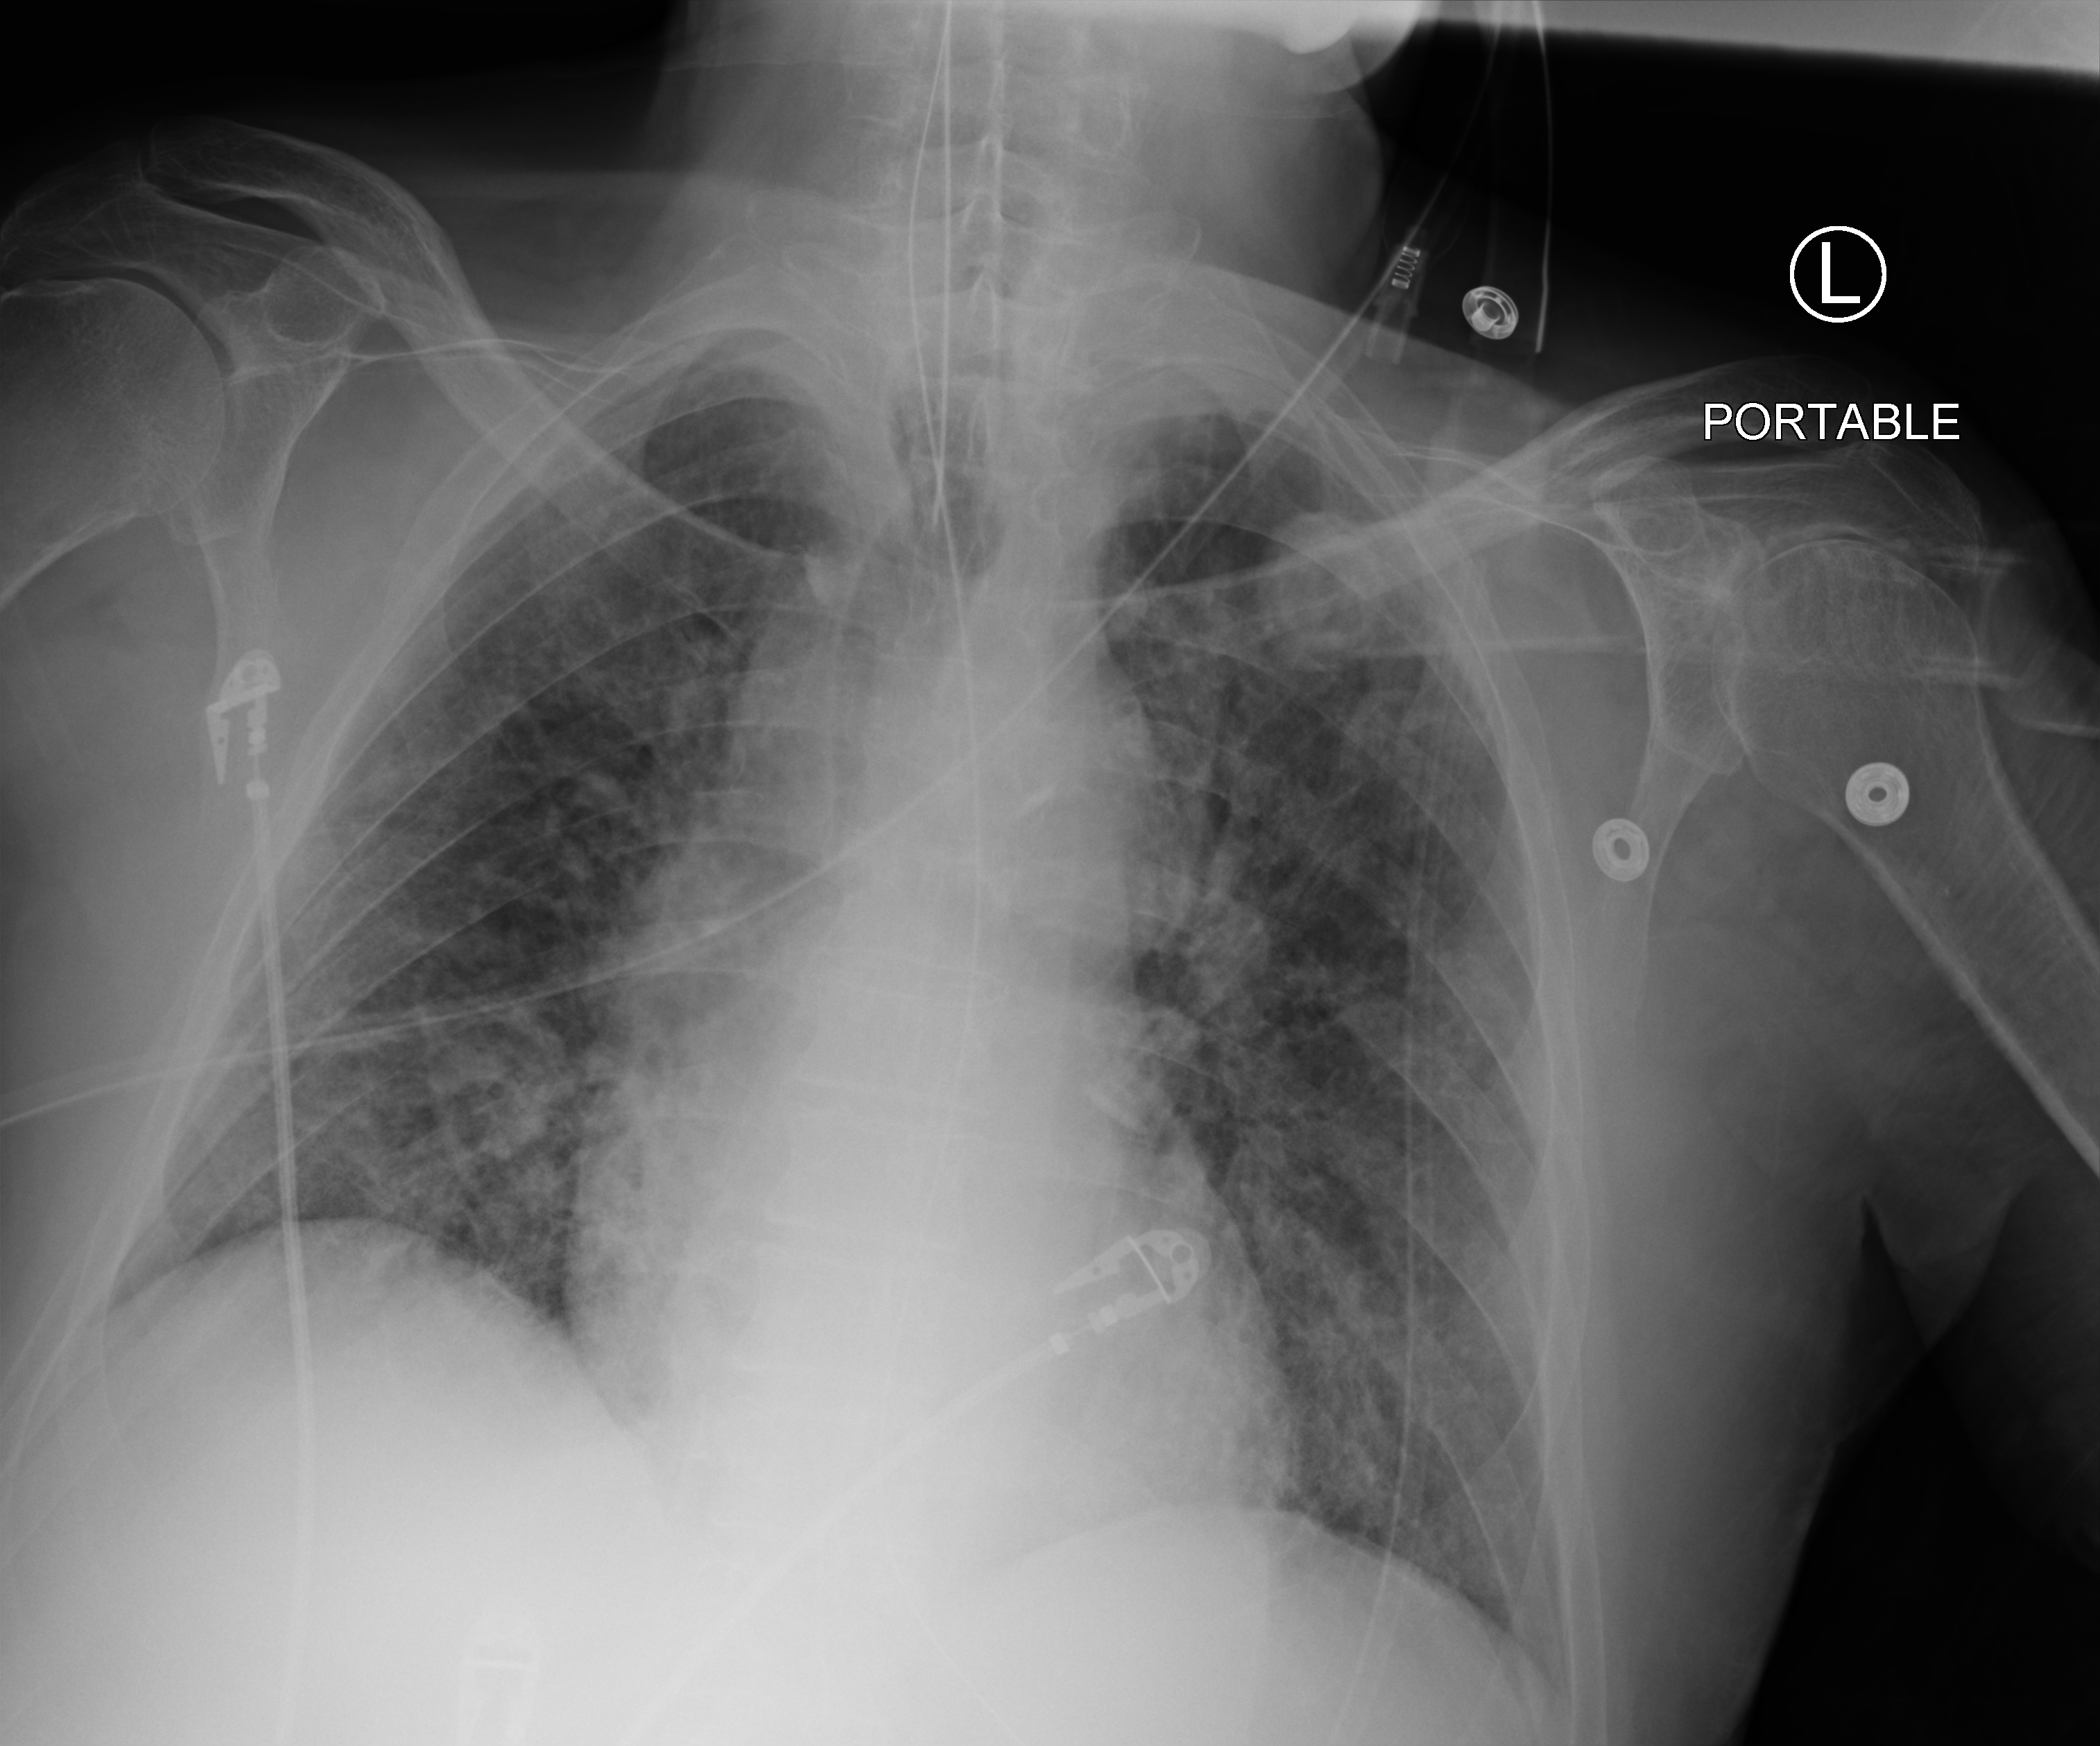
Portable chest radiograph, anteroposterior (AP) projection. Patient hospitalised with COVID-19; male, aged 60–74 years.
Admission-level facts for this patient (not findings on this image; timing relative to this image not recorded):
- admitted to intensive care during this hospital stay: yes
- COPD (admission record): no